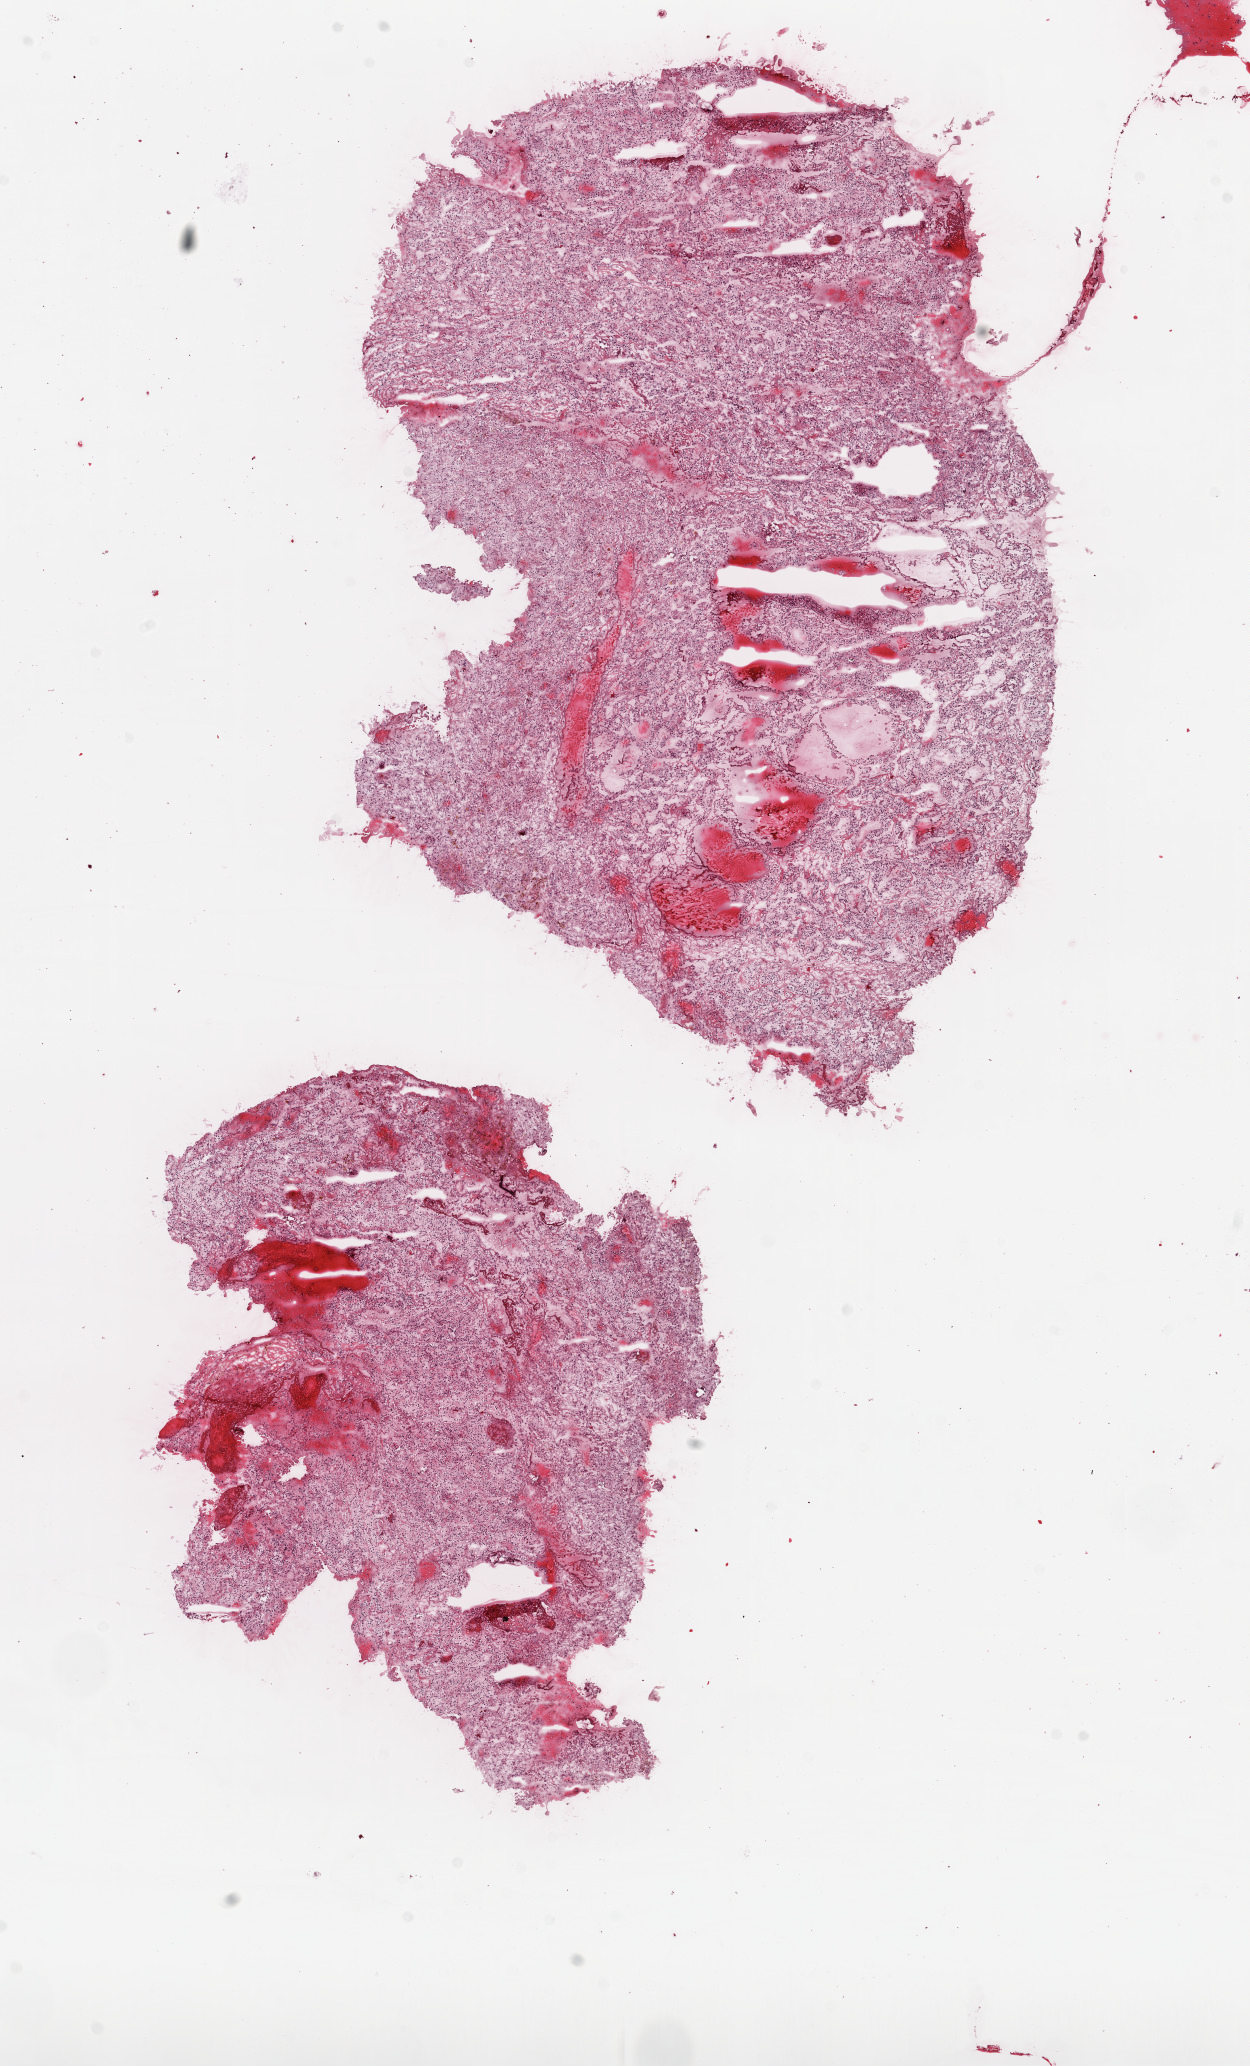
Digitized H&E-stained tissue section (whole slide), low-resolution overview of the scanned area, about 10.0 x 16.6 mm; frozen section from the top of the tissue portion; primary tumour sample from the kidney. Male patient; age at initial diagnosis 78 years. Histologic grade: G3 (poorly differentiated). Composition of this section per pathologist review: tumour cells 100%, tumour nuclei 95%, necrosis 0%. Inflammatory infiltration, as recorded: lymphocyte infiltration 1%.
- AJCC pathologic stage: I
- diagnosis: Clear cell adenocarcinoma, NOS
- laterality: right